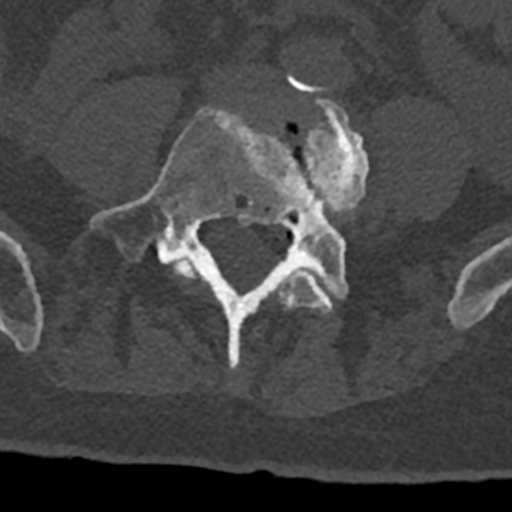
CT including the spine, one axial slice. Slice 217 of 797 in the series (ordered by position). Reconstruction kernel Br40s/3. 120 kVp. Bone window (W 1800 / L 400 HU). 0.5 mm slice thickness. 512 × 512 image matrix, field of view 160 × 160 mm. Male patient, age 74 years. From the clinical record (not read from this slice): primary cancer: renal; vertebrae with lytic lesions (as recorded): T10, L1, L2, L3, L4, L5.
Outlined on this slice (semi-automatic segmentation, software-assisted and operator-edited):
- L4 vertebra: bounding box [x1, y1, x2, y2] px = [173, 94, 369, 315]
- L5 vertebra: [90, 108, 348, 367]